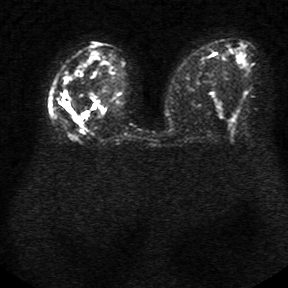
Breast MRI, one axial slice; position 13 of 34 along the scan axis; diffusion-weighted series; image 2 of 4 stored at this slice position (different b-values; order by instance number); 1.5 T; 5 mm slice thickness; 288 × 288 image matrix, field of view 340 × 340 mm. Female patient.
Annotated regions visible in this slice (expert manual segmentation):
- tumour on diffusion-weighted imaging: bounding box [x1, y1, x2, y2] px = [80, 100, 107, 122]